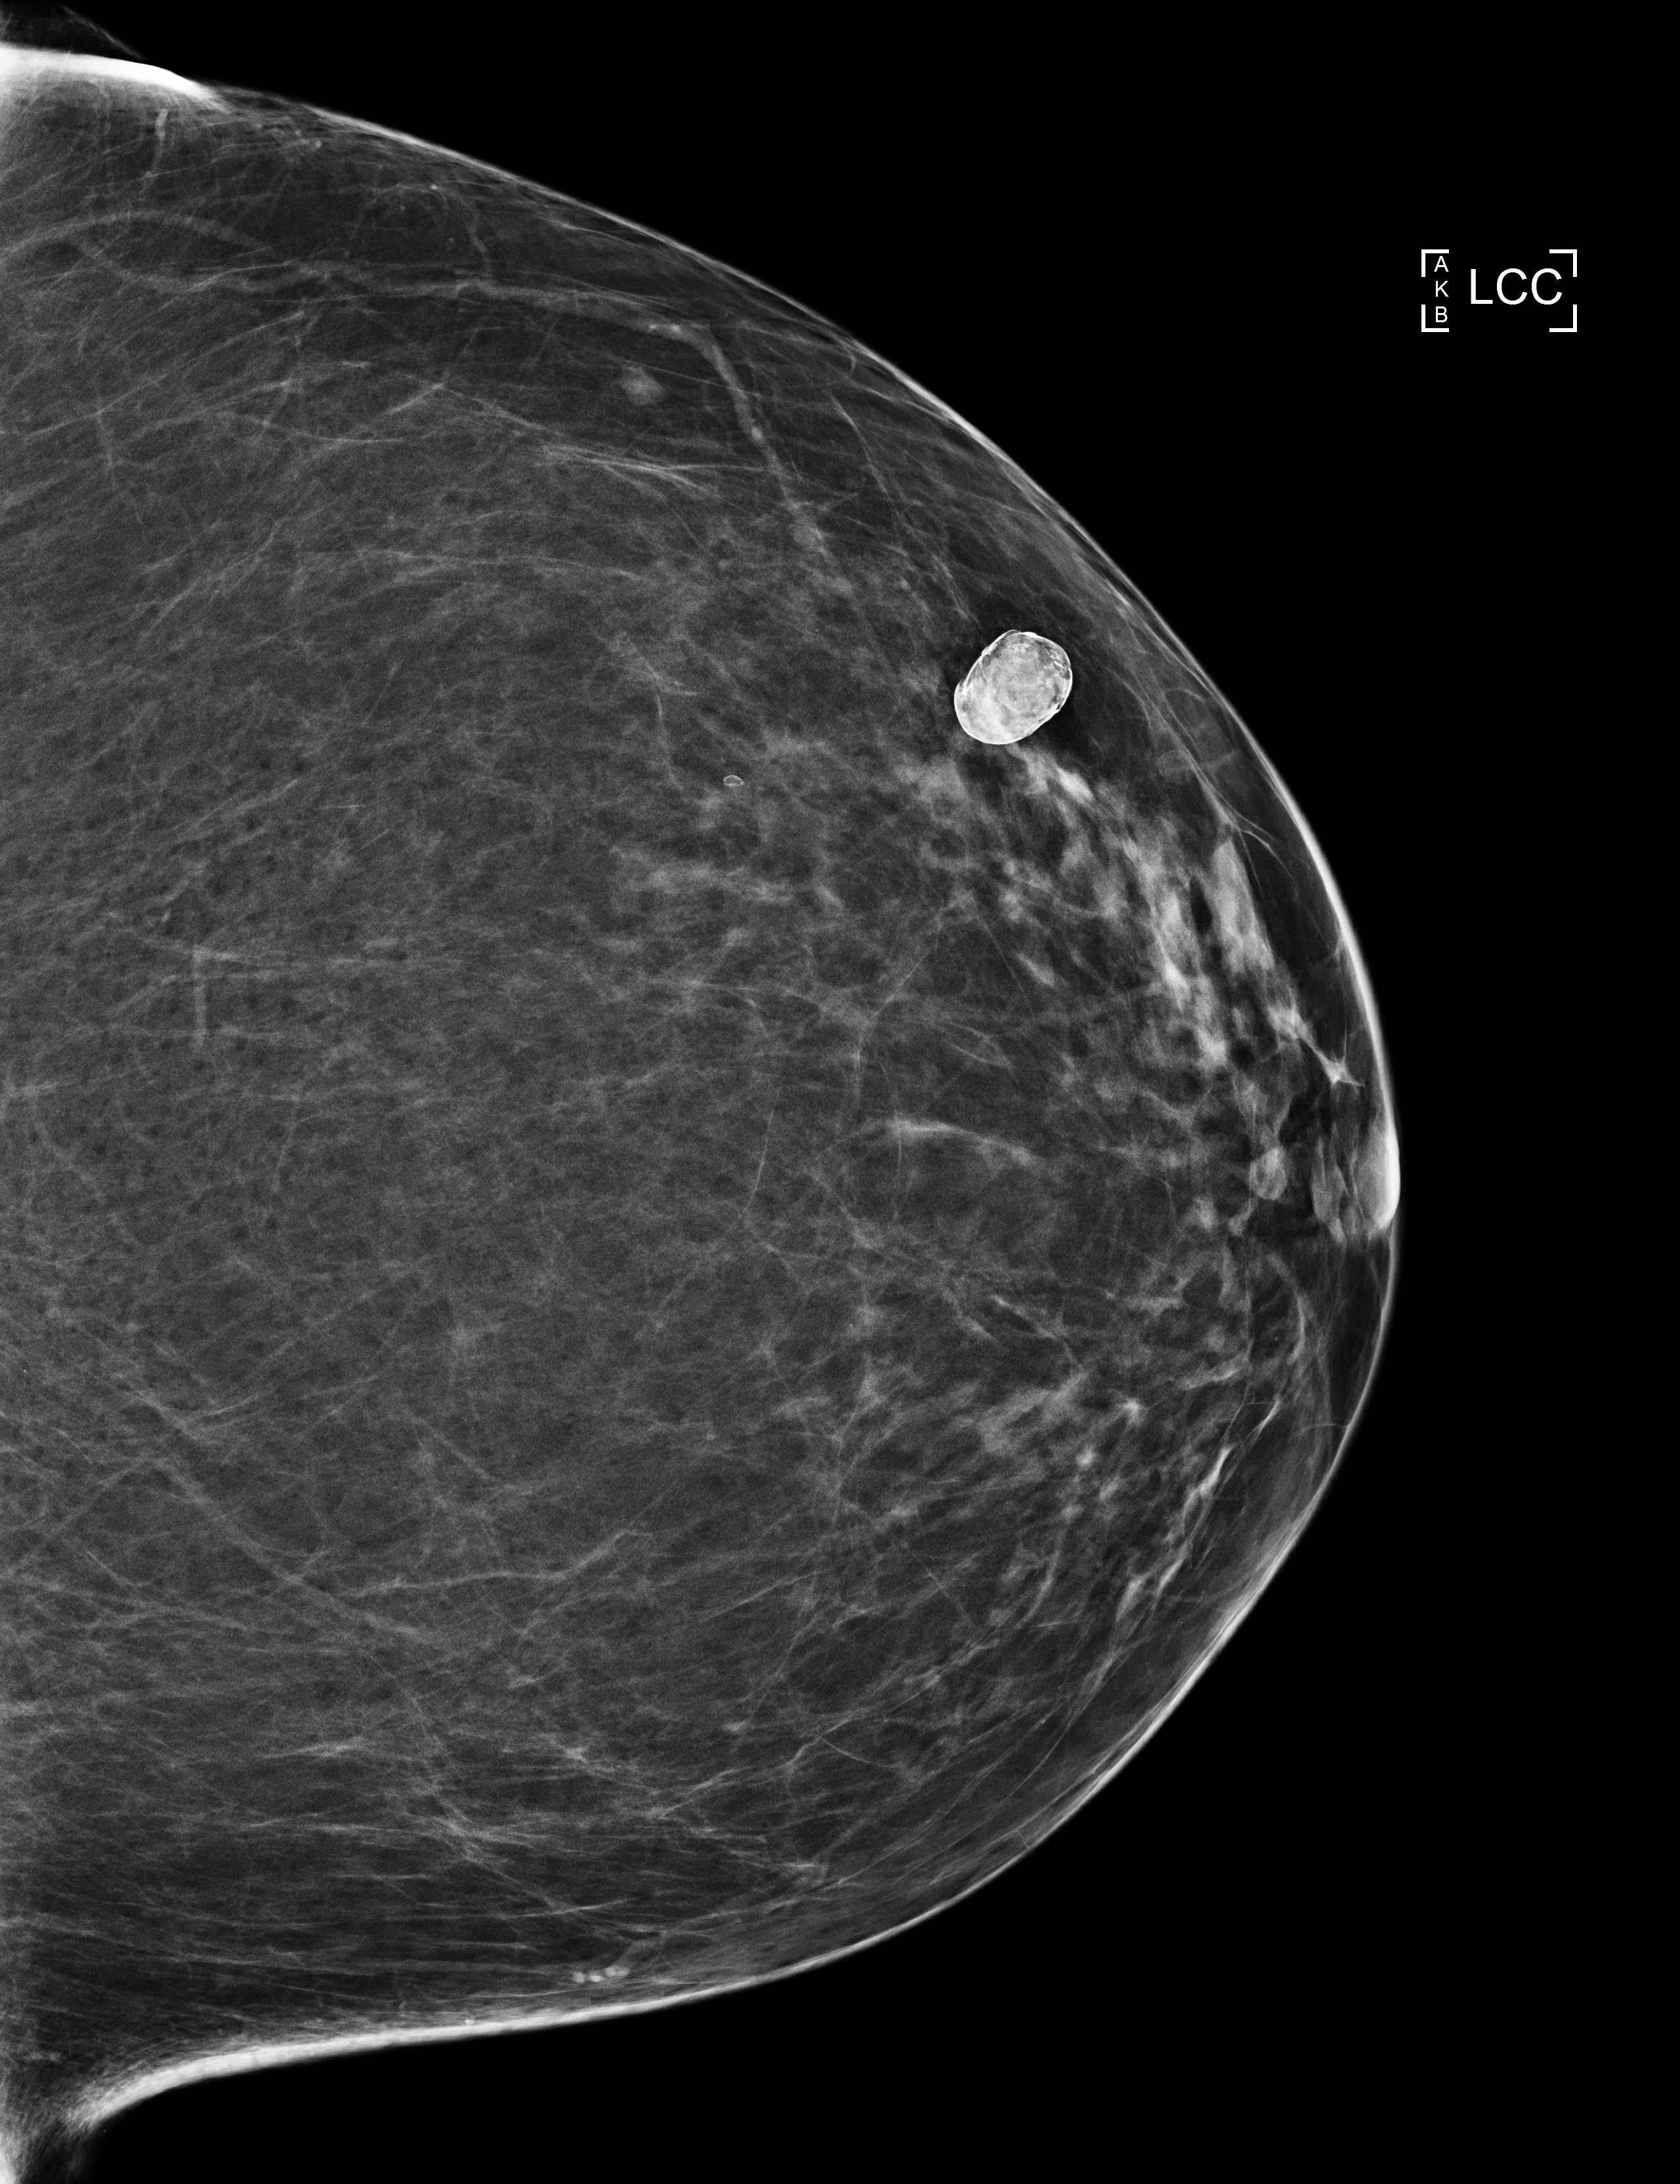
Screening examination, system: Selenia Dimensions. Patient aged 66 years (female).
Image type: full-field digital mammogram. Breast: left. Projection: cranio-caudal projection. BI-RADS breast density category at the screening exam (both breasts, scale 1–4): 2. Final BI-RADS assessment for this screening round (tomosynthesis exam, both breasts): category 1. Recall: no recall after this screen.